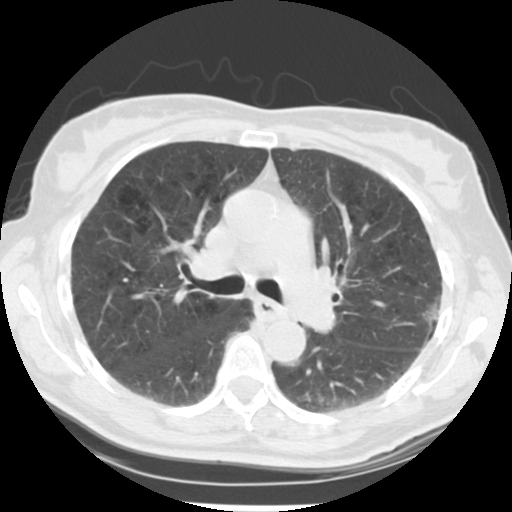
Low-dose screening chest CT, axial slice. Second screening round (one year after baseline). Lung window (W 1500 / L -600 HU). Standard (soft-tissue) reconstruction kernel (STANDARD). Slice 137 of 223 in the series. 512 × 512 image matrix. Female, age 61 years at enrolment.
Expert reader's lesion annotation, bounding box <406,282,464,344> (left, top, right, bottom; pixels). Reader record for this screening exam (exam-level; its link to the box is not recorded): non-calcified nodule or mass ≥4 mm, left upper lobe, 15 × 15 mm, poorly defined margins, mixed attenuation, pre-existing on the prior screen: no. Participant outcome: lung cancer diagnosed 152 days after this screen — bronchiolo-alveolar adenocarcinoma, NOS, left upper lobe, well differentiated (G1), stage IA (AJCC 6th edition), 11 mm at pathology.